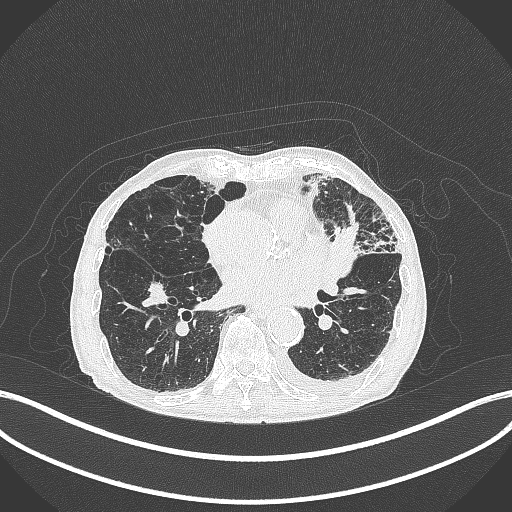
Chest CT, one axial slice; position 160 of 385 along the scan axis; reconstruction kernel B70f; 120 kVp; lung window (W 1500 / L -600 HU); 1 mm slice thickness; 512 × 512 image matrix, field of view 400 × 400 mm. Patient: male, 90 years or older. From the clinical record (not read from this slice): clinical TNM (as recorded): T2b N1 M0.
Outlined on this slice (rectangle marked by the reading radiologist):
- lung tumour (recorded histology: squamous cell carcinoma): bounding box <327,221,360,278> (left, top, right, bottom; pixels)